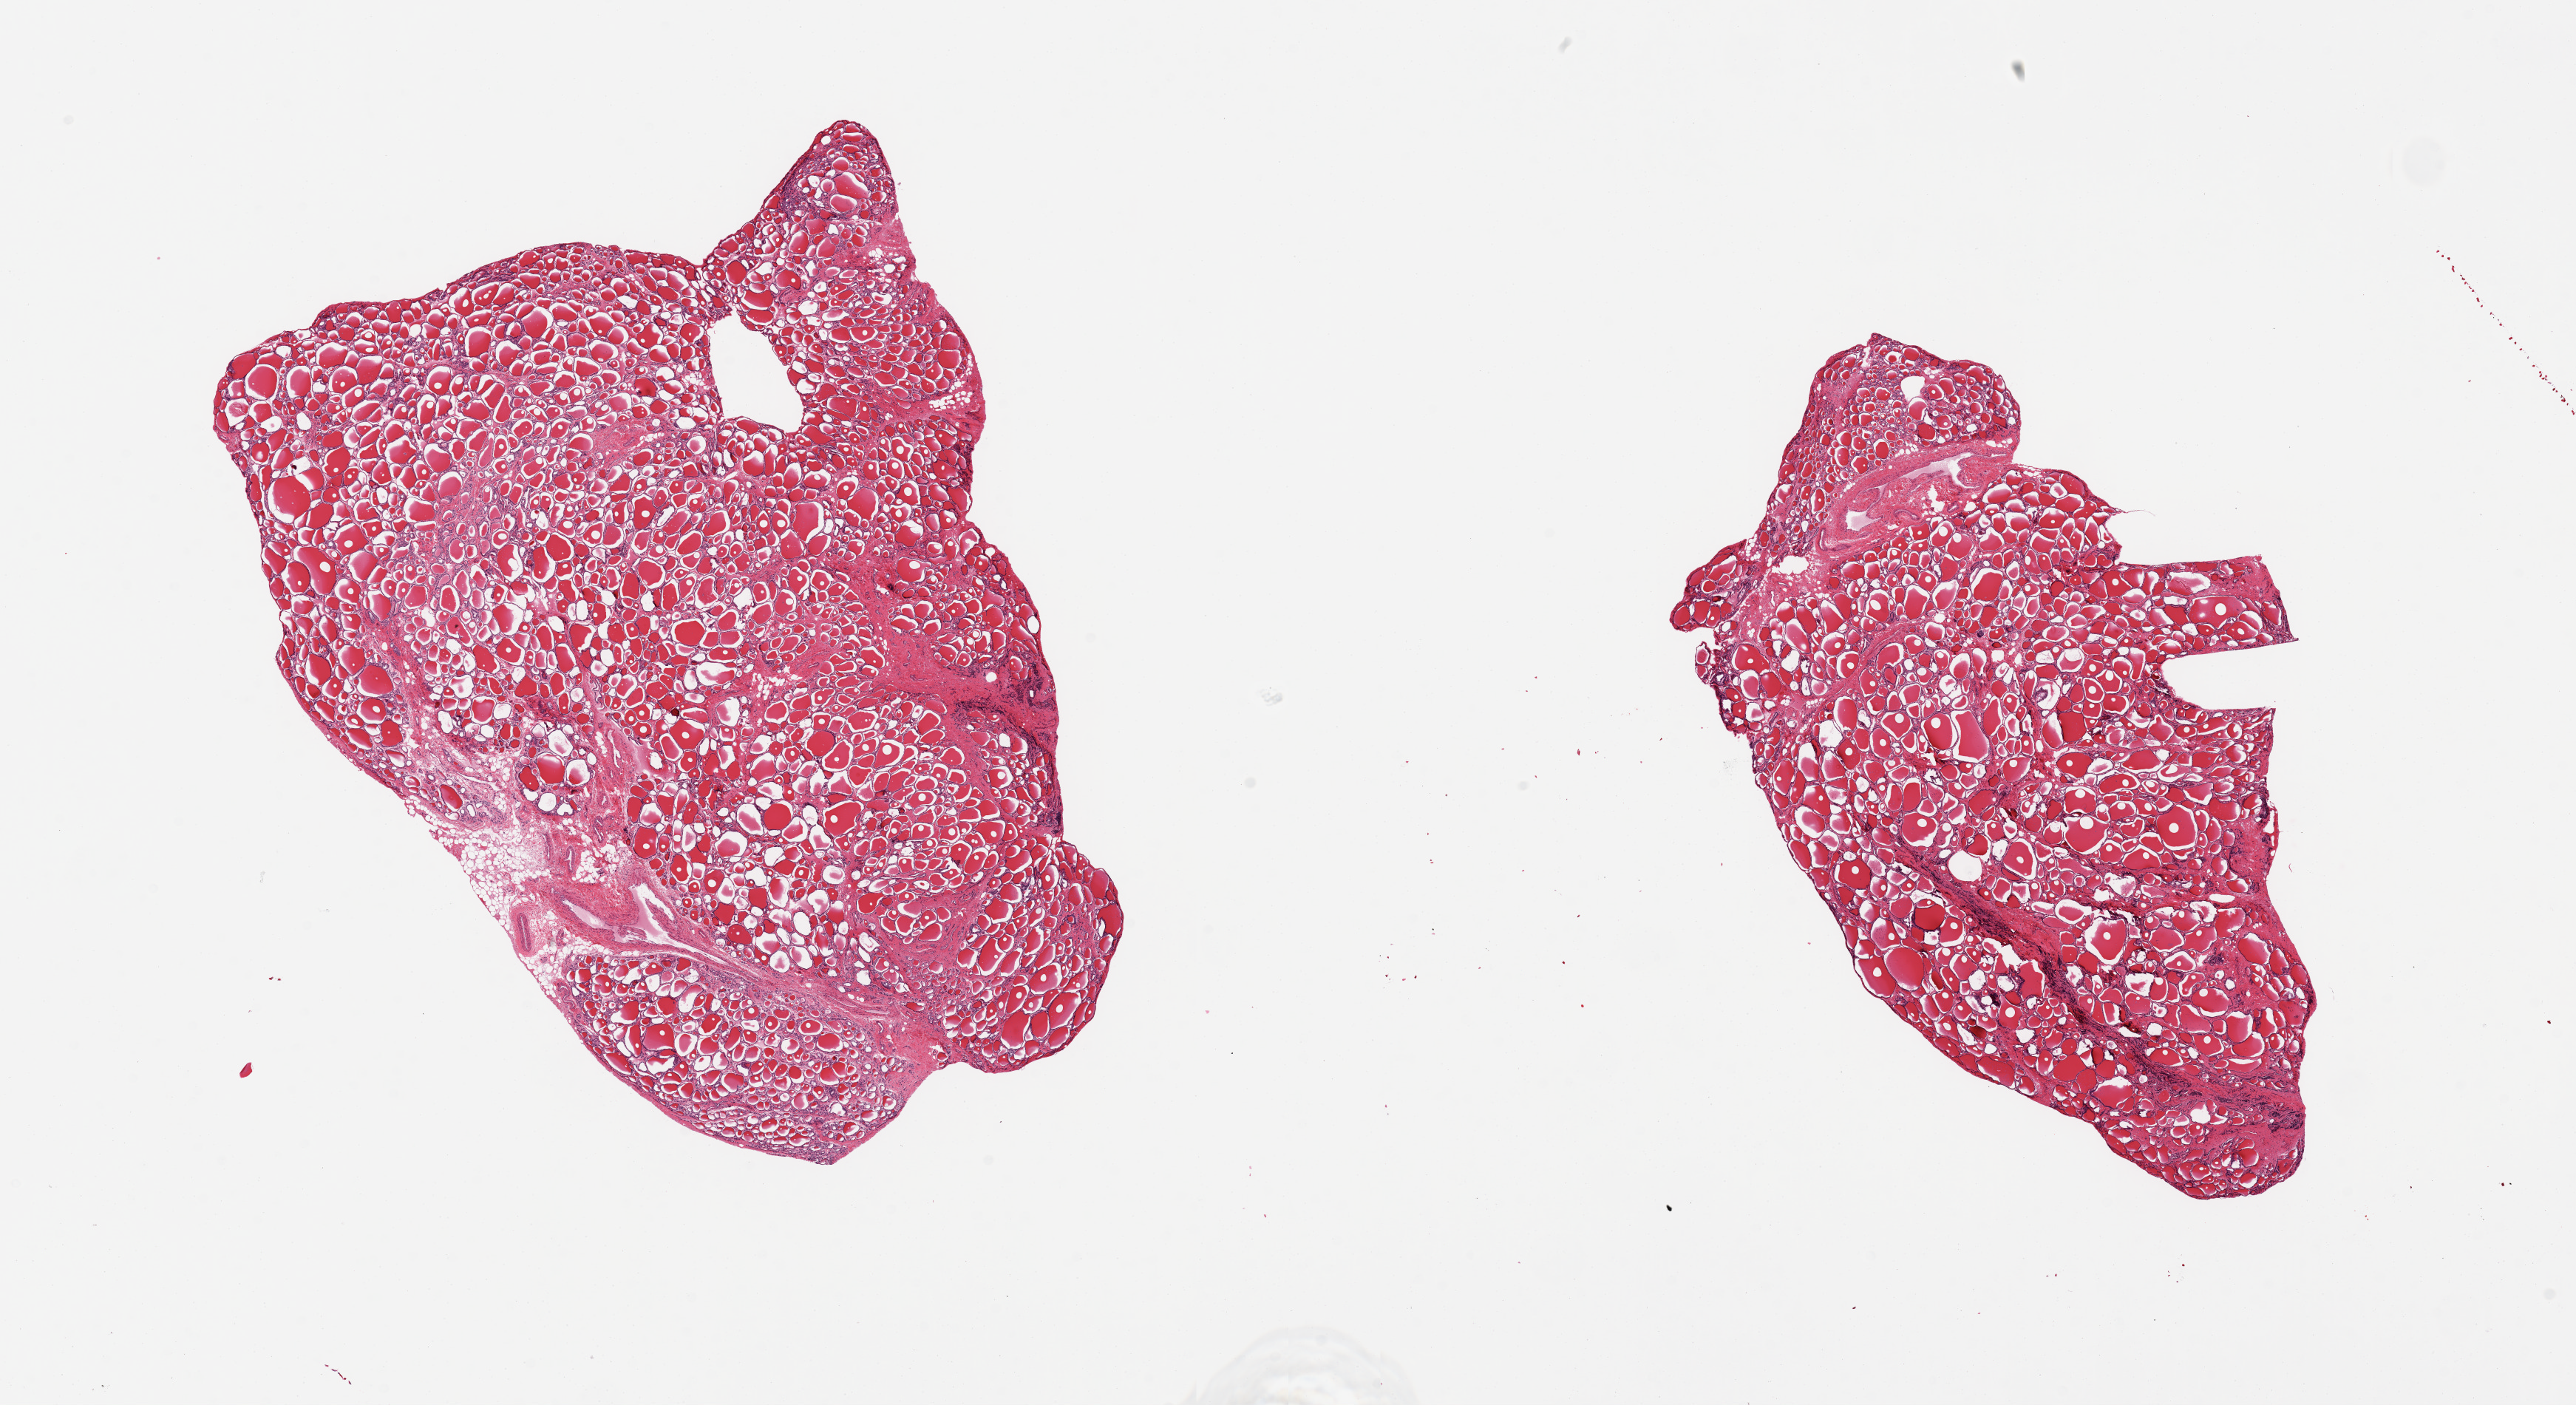
Haematoxylin and eosin whole-slide image, brightfield — whole scanned area (about 27.6 x 15.0 mm) shown as a low-resolution overview; PAXgene-fixed, paraffin-embedded tissue; target tissue: thyroid; tissue donor sample.
Pathologist's review note for this sample: 2 pieces.